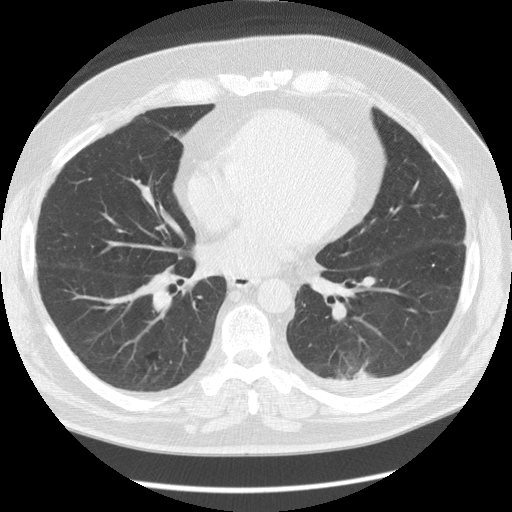
Low-dose screening chest CT, one axial slice. Slice 59 of 126 in the series (ordered by position). Reconstruction kernel STANDARD. 120 kVp. Lung window (W 1500 / L -600 HU). 2.5 mm slice thickness. 512 × 512 image matrix.
Annotated regions visible in this slice (expert manual segmentation):
- lesion 1 (tumor, lower lobe of left lung): bounding box <354,364,373,379> (left, top, right, bottom; pixels)